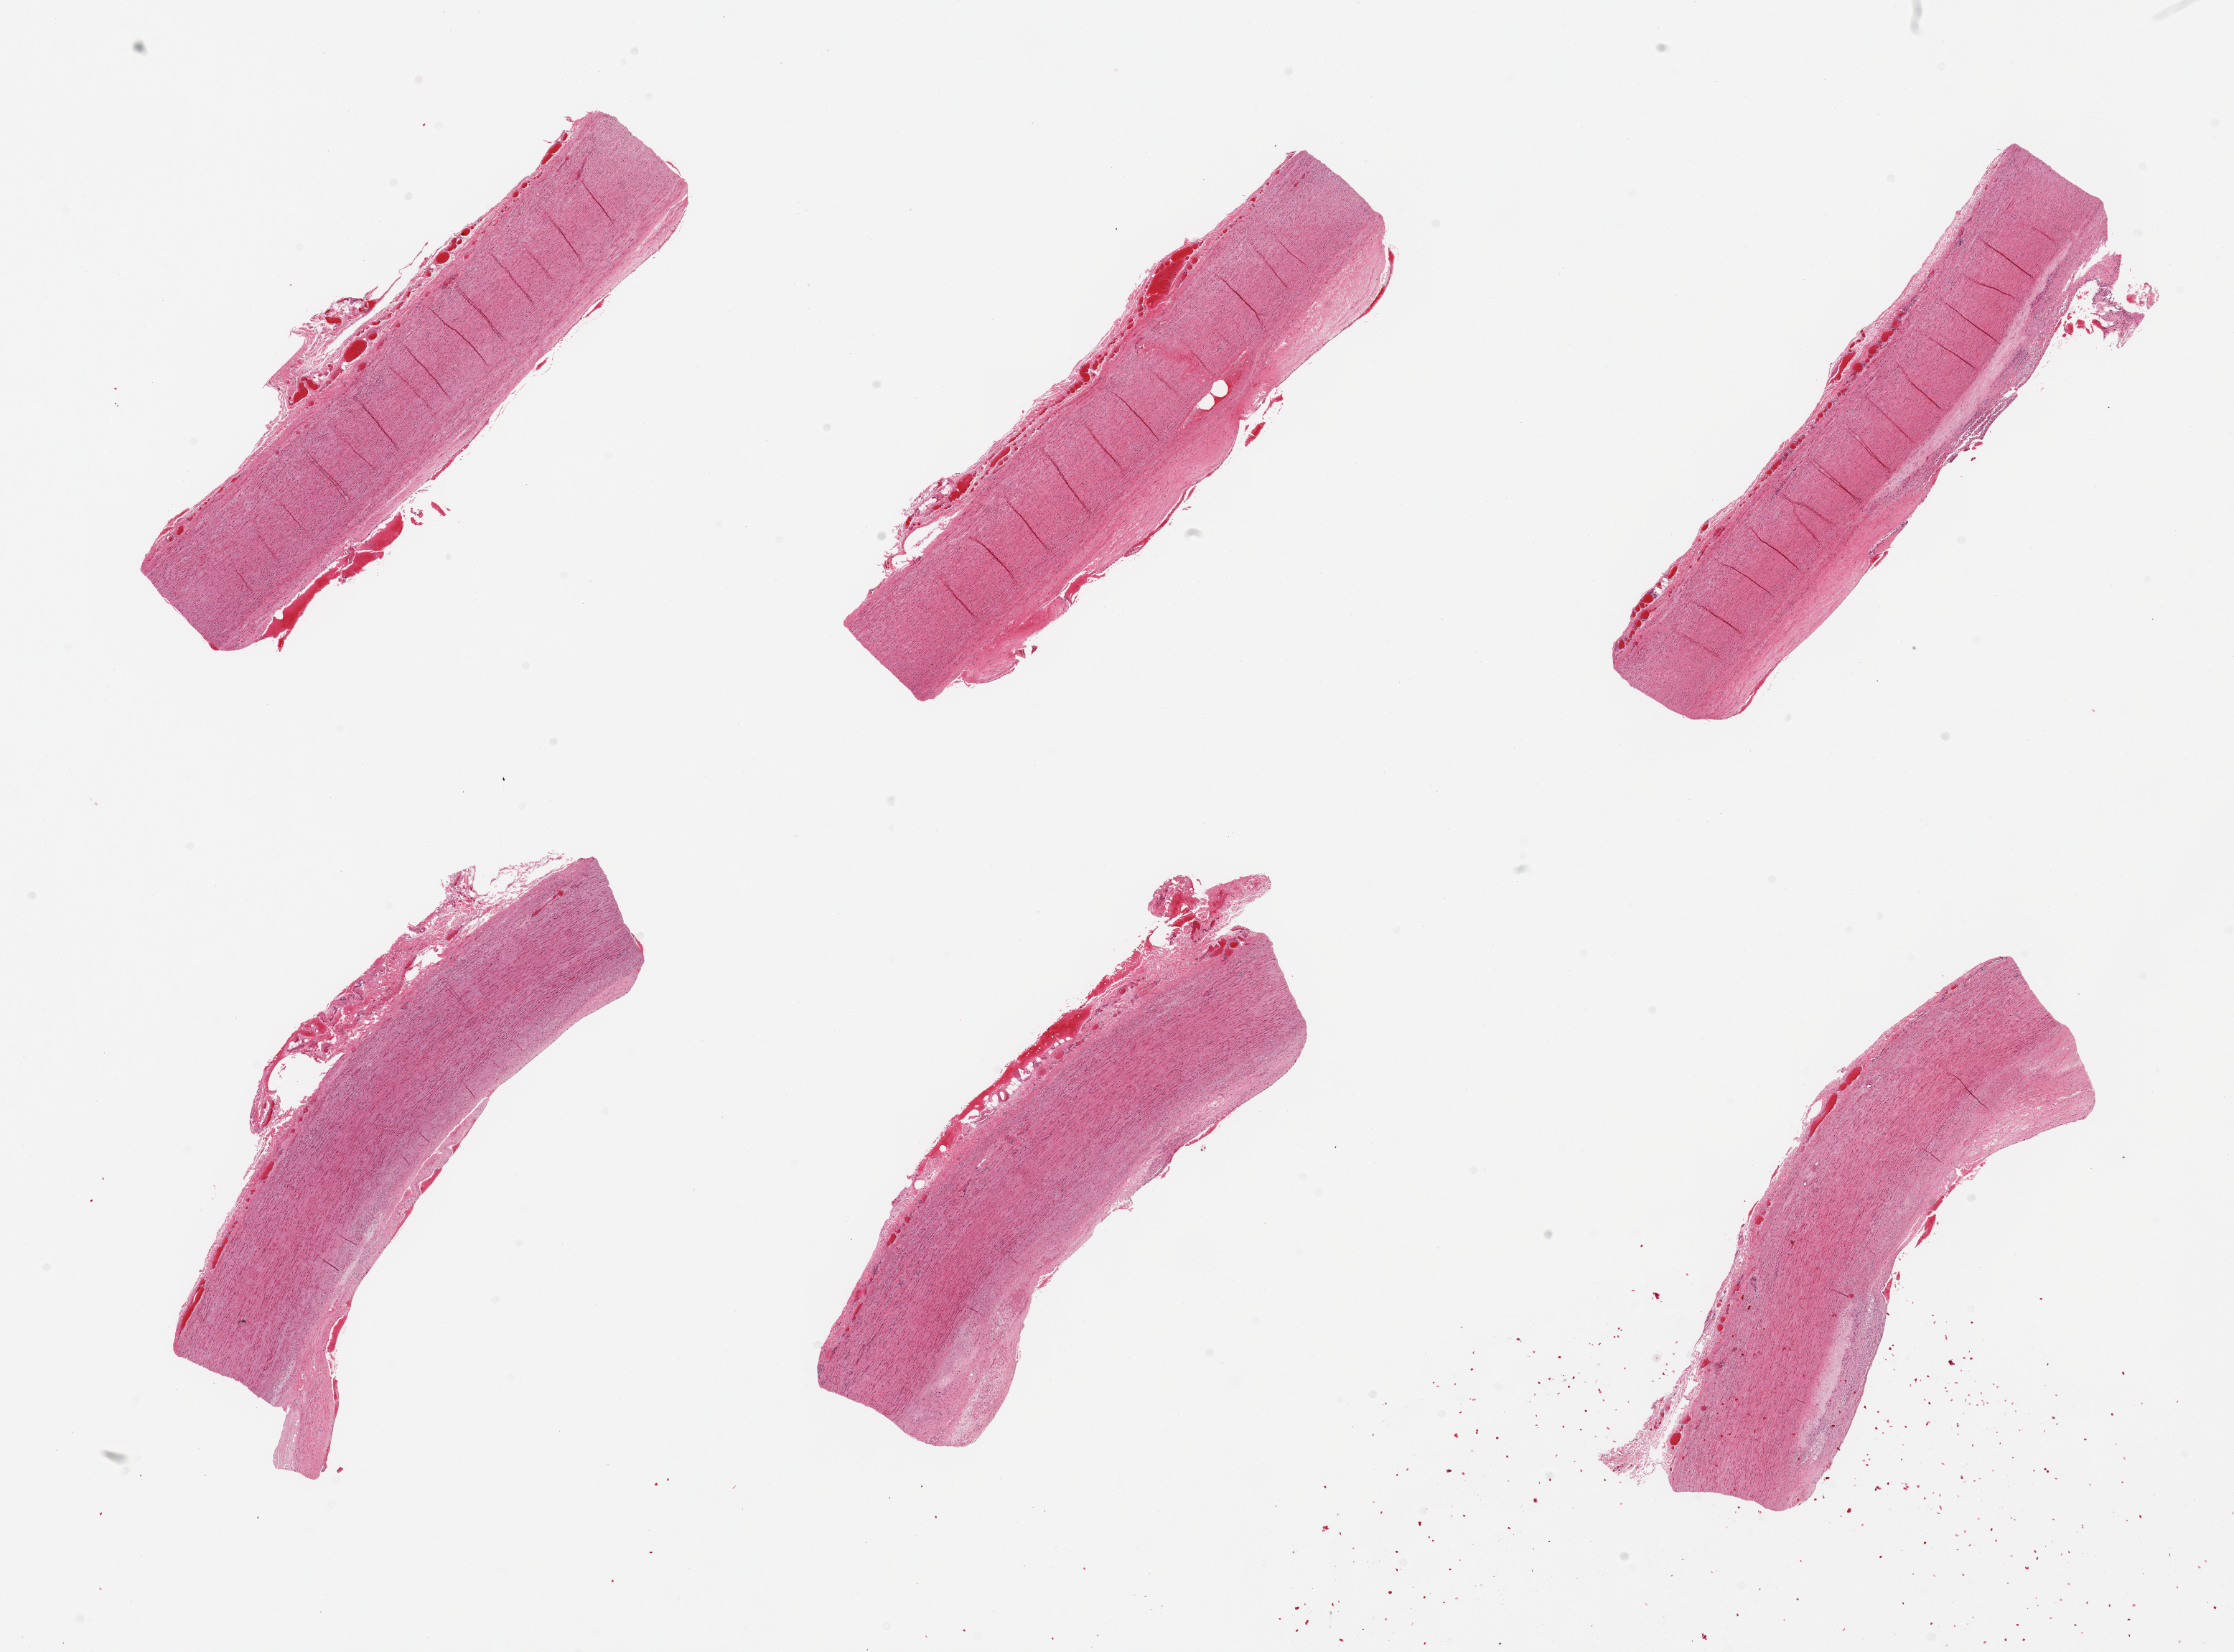
Digitized haematoxylin and eosin-stained section, whole scanned area (about 24.6 x 18.2 mm) shown as a low-resolution overview; PAXgene-fixed paraffin-embedded (PFPE) section; section of aorta (target tissue); tissue donor sample. Donor sex: male.
Review note (as recorded): 6 pieces, atherosis up to ~0.8mm.